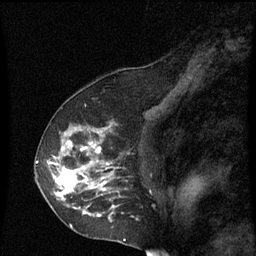
Breast MRI (dynamic contrast-enhanced), one sagittal slice; position 40 of 60 along the scan axis; dynamic contrast-enhanced series, image 2 of 3 at this slice position (ordered by acquisition); 1.5 T; TE 4.2 ms, TR 8.9 ms; 2 mm slice thickness; 256 × 256 image matrix, field of view 200 × 200 mm. Patient: female, 53 years. From the clinical record (not read from this slice): setting: breast cancer imaged before/during neoadjuvant chemotherapy; receptor status: HR-positive, HER2-negative.
Outlined on this slice (semi-automatically segmented with operator editing):
- analysis volume of interest (the breast-tissue region the enhancement analysis was run in; not a lesion): bounding box [x1, y1, x2, y2] px = [38, 128, 121, 231]
- tumour enhancement mask (voxels above the 70 % enhancement threshold inside the analysis volume of interest): [50, 128, 115, 217]